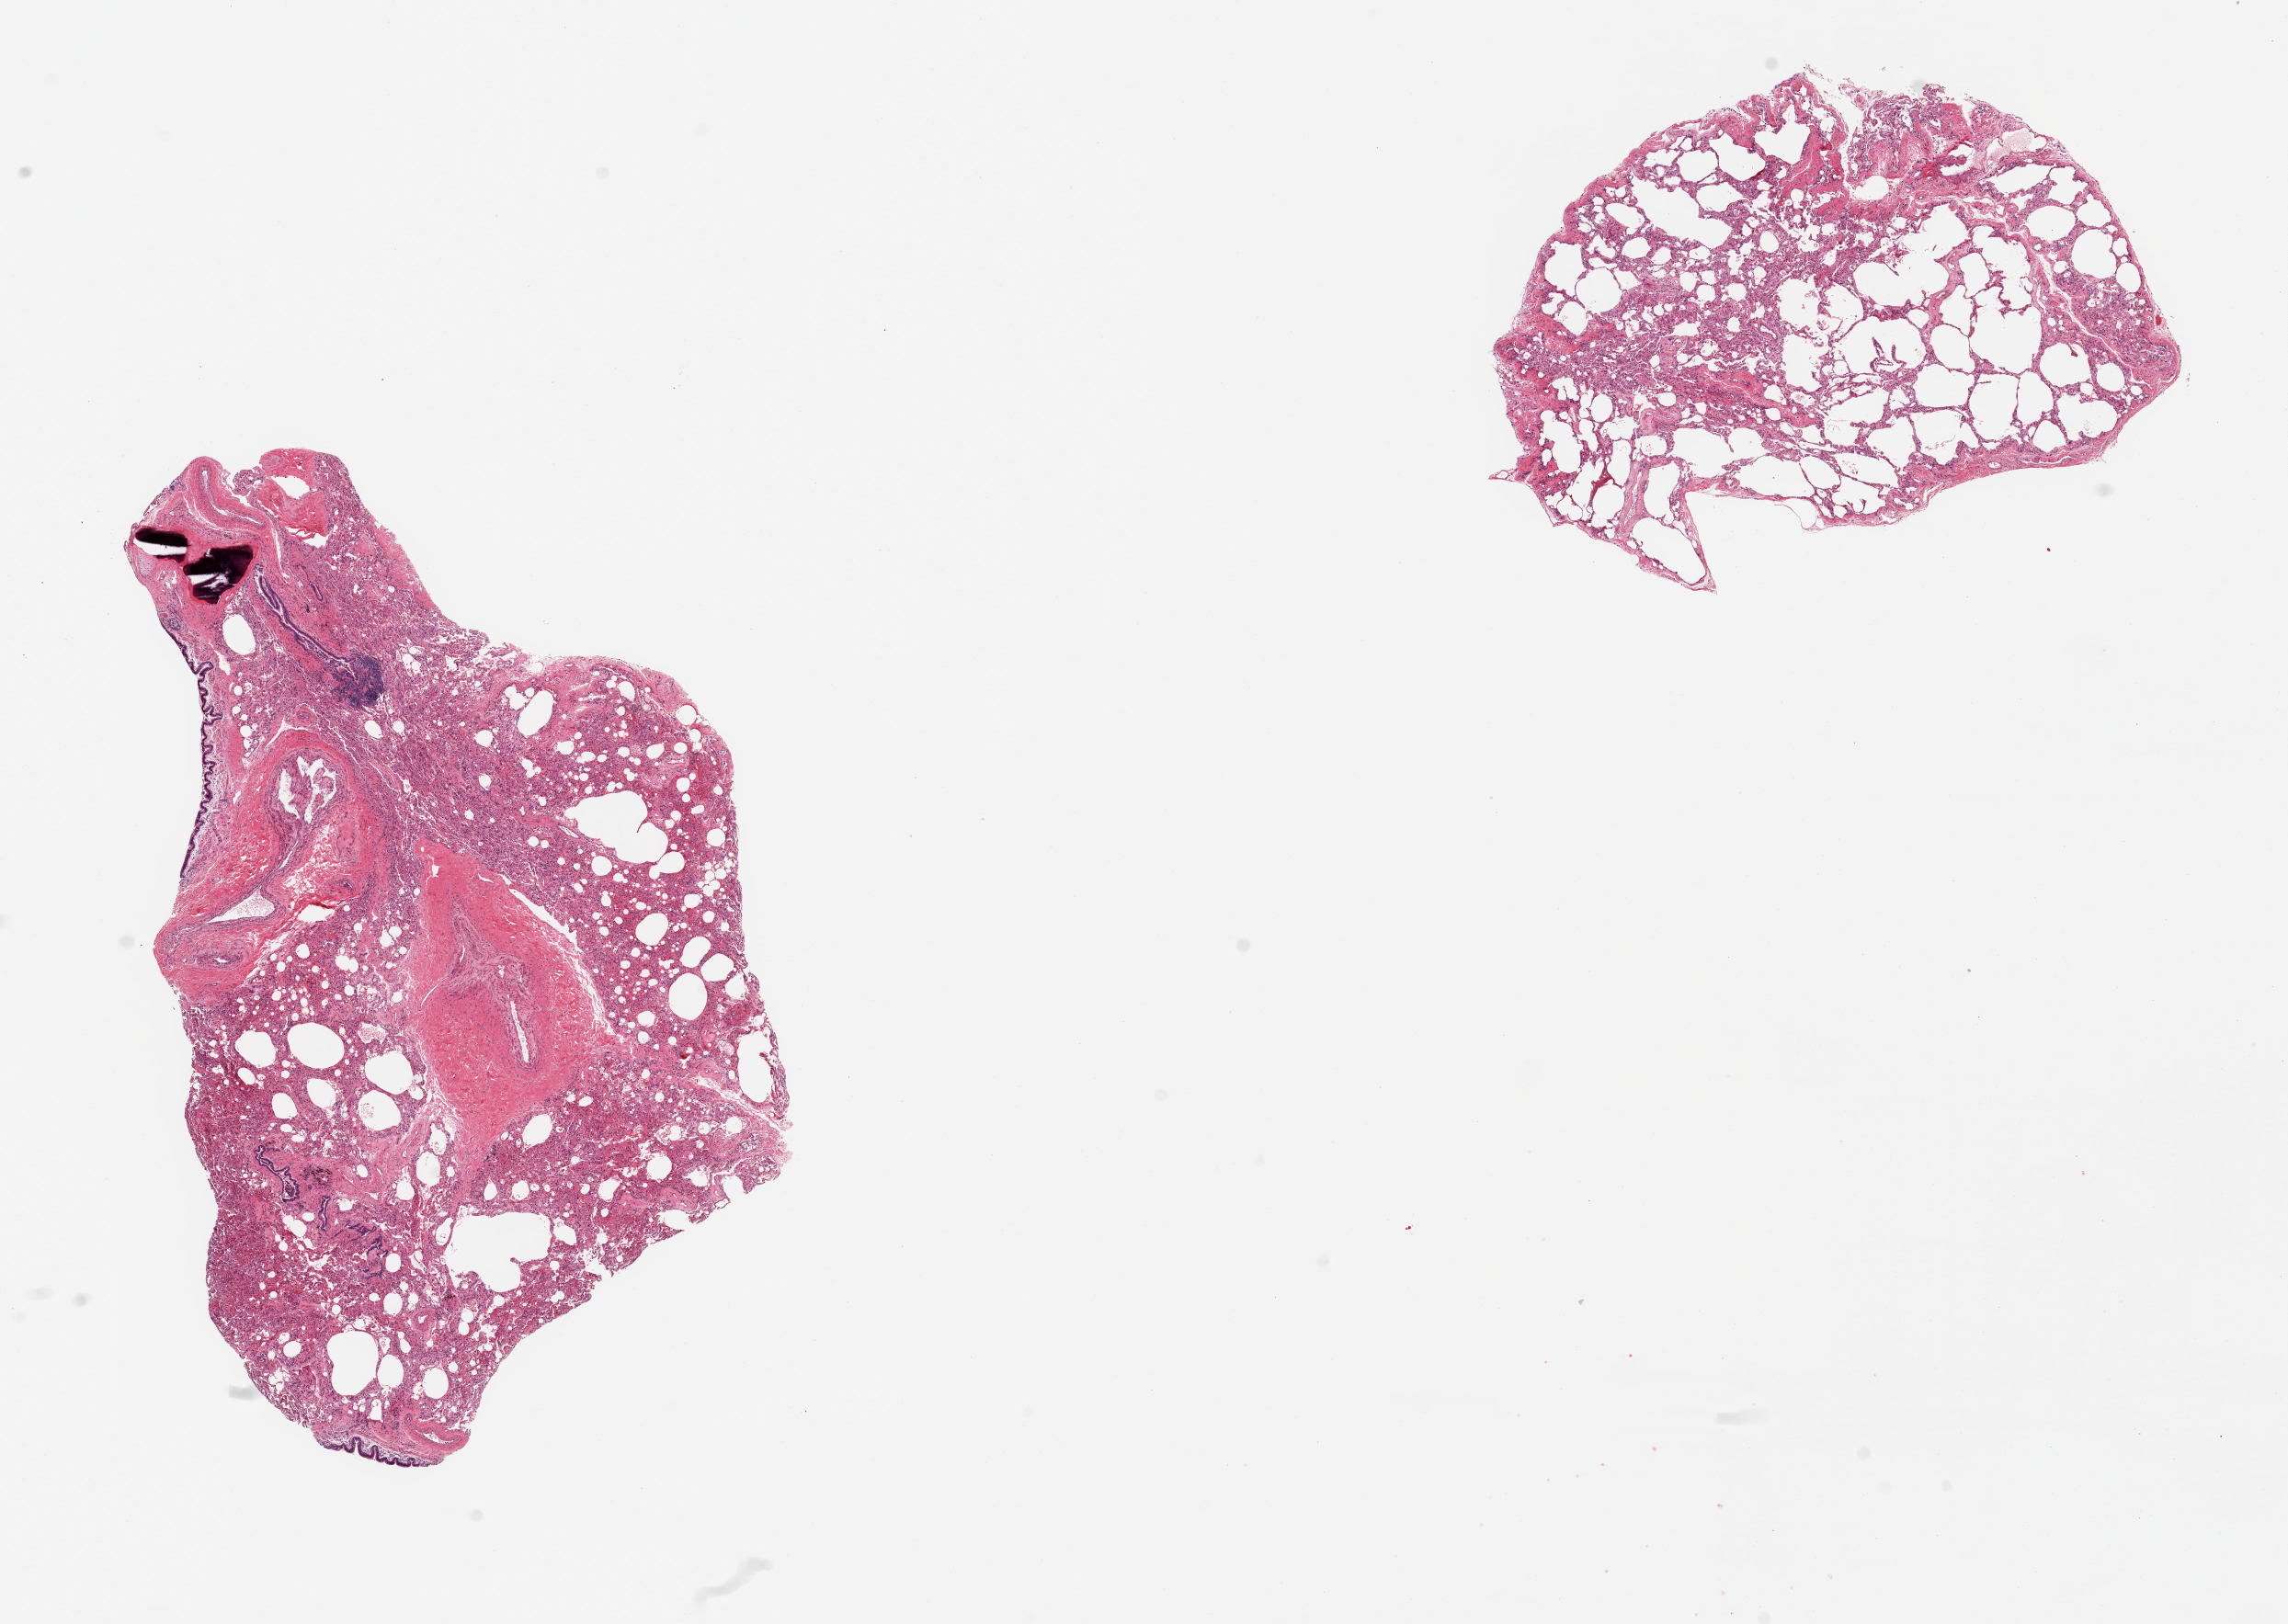
Whole-slide image, haematoxylin and eosin stain, brightfield, shown as a low-resolution overview of the whole scanned area (about 19.7 x 14.0 mm), PAXgene-fixed paraffin-embedded (PFPE) section, section of lung (target tissue), tissue donor sample. Male donor.
• review note (as recorded): 2 pieces; emphysema; large calcified bronchus and vessels comprise 30% of 1 piece